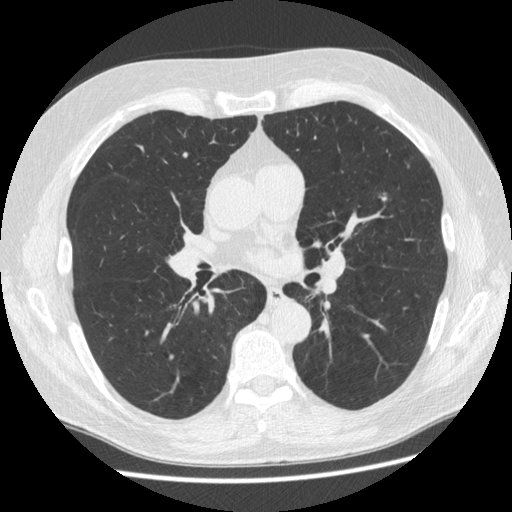
Low-dose screening chest CT, one axial slice; reconstruction kernel STANDARD; 120 kVp; lung window (W 1500 / L -600 HU); 512 × 512 image matrix, field of view 360 × 360 mm.
Annotated regions visible in this slice (expert manual segmentation):
- lesion 1 (nodule, upper lobe of left lung): bounding box <382,197,386,201> (left, top, right, bottom; pixels)